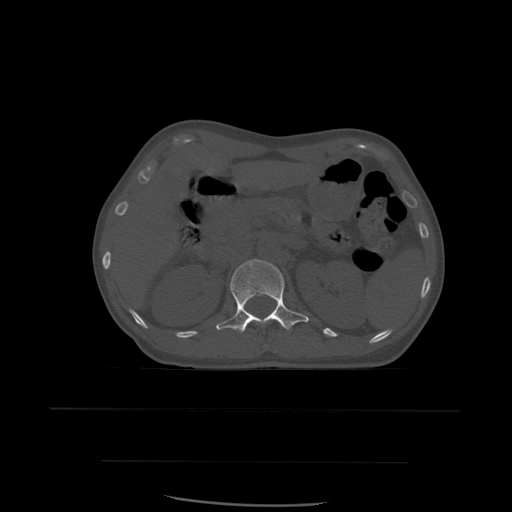
CT including the spine, one axial slice. Position 251 of 574 along the scan axis. Bone window (W 1800 / L 400 HU). 1.25 mm slice thickness. 512 × 512 image matrix, field of view 392 × 392 mm. Patient age 48 years. From the clinical record (not read from this slice): primary cancer: lung; vertebrae with lytic lesions (as recorded): T11.
Annotated regions visible in this slice (semi-automatically segmented with operator editing):
- L1 vertebra: bounding box [x1, y1, x2, y2] px = [216, 259, 309, 334]